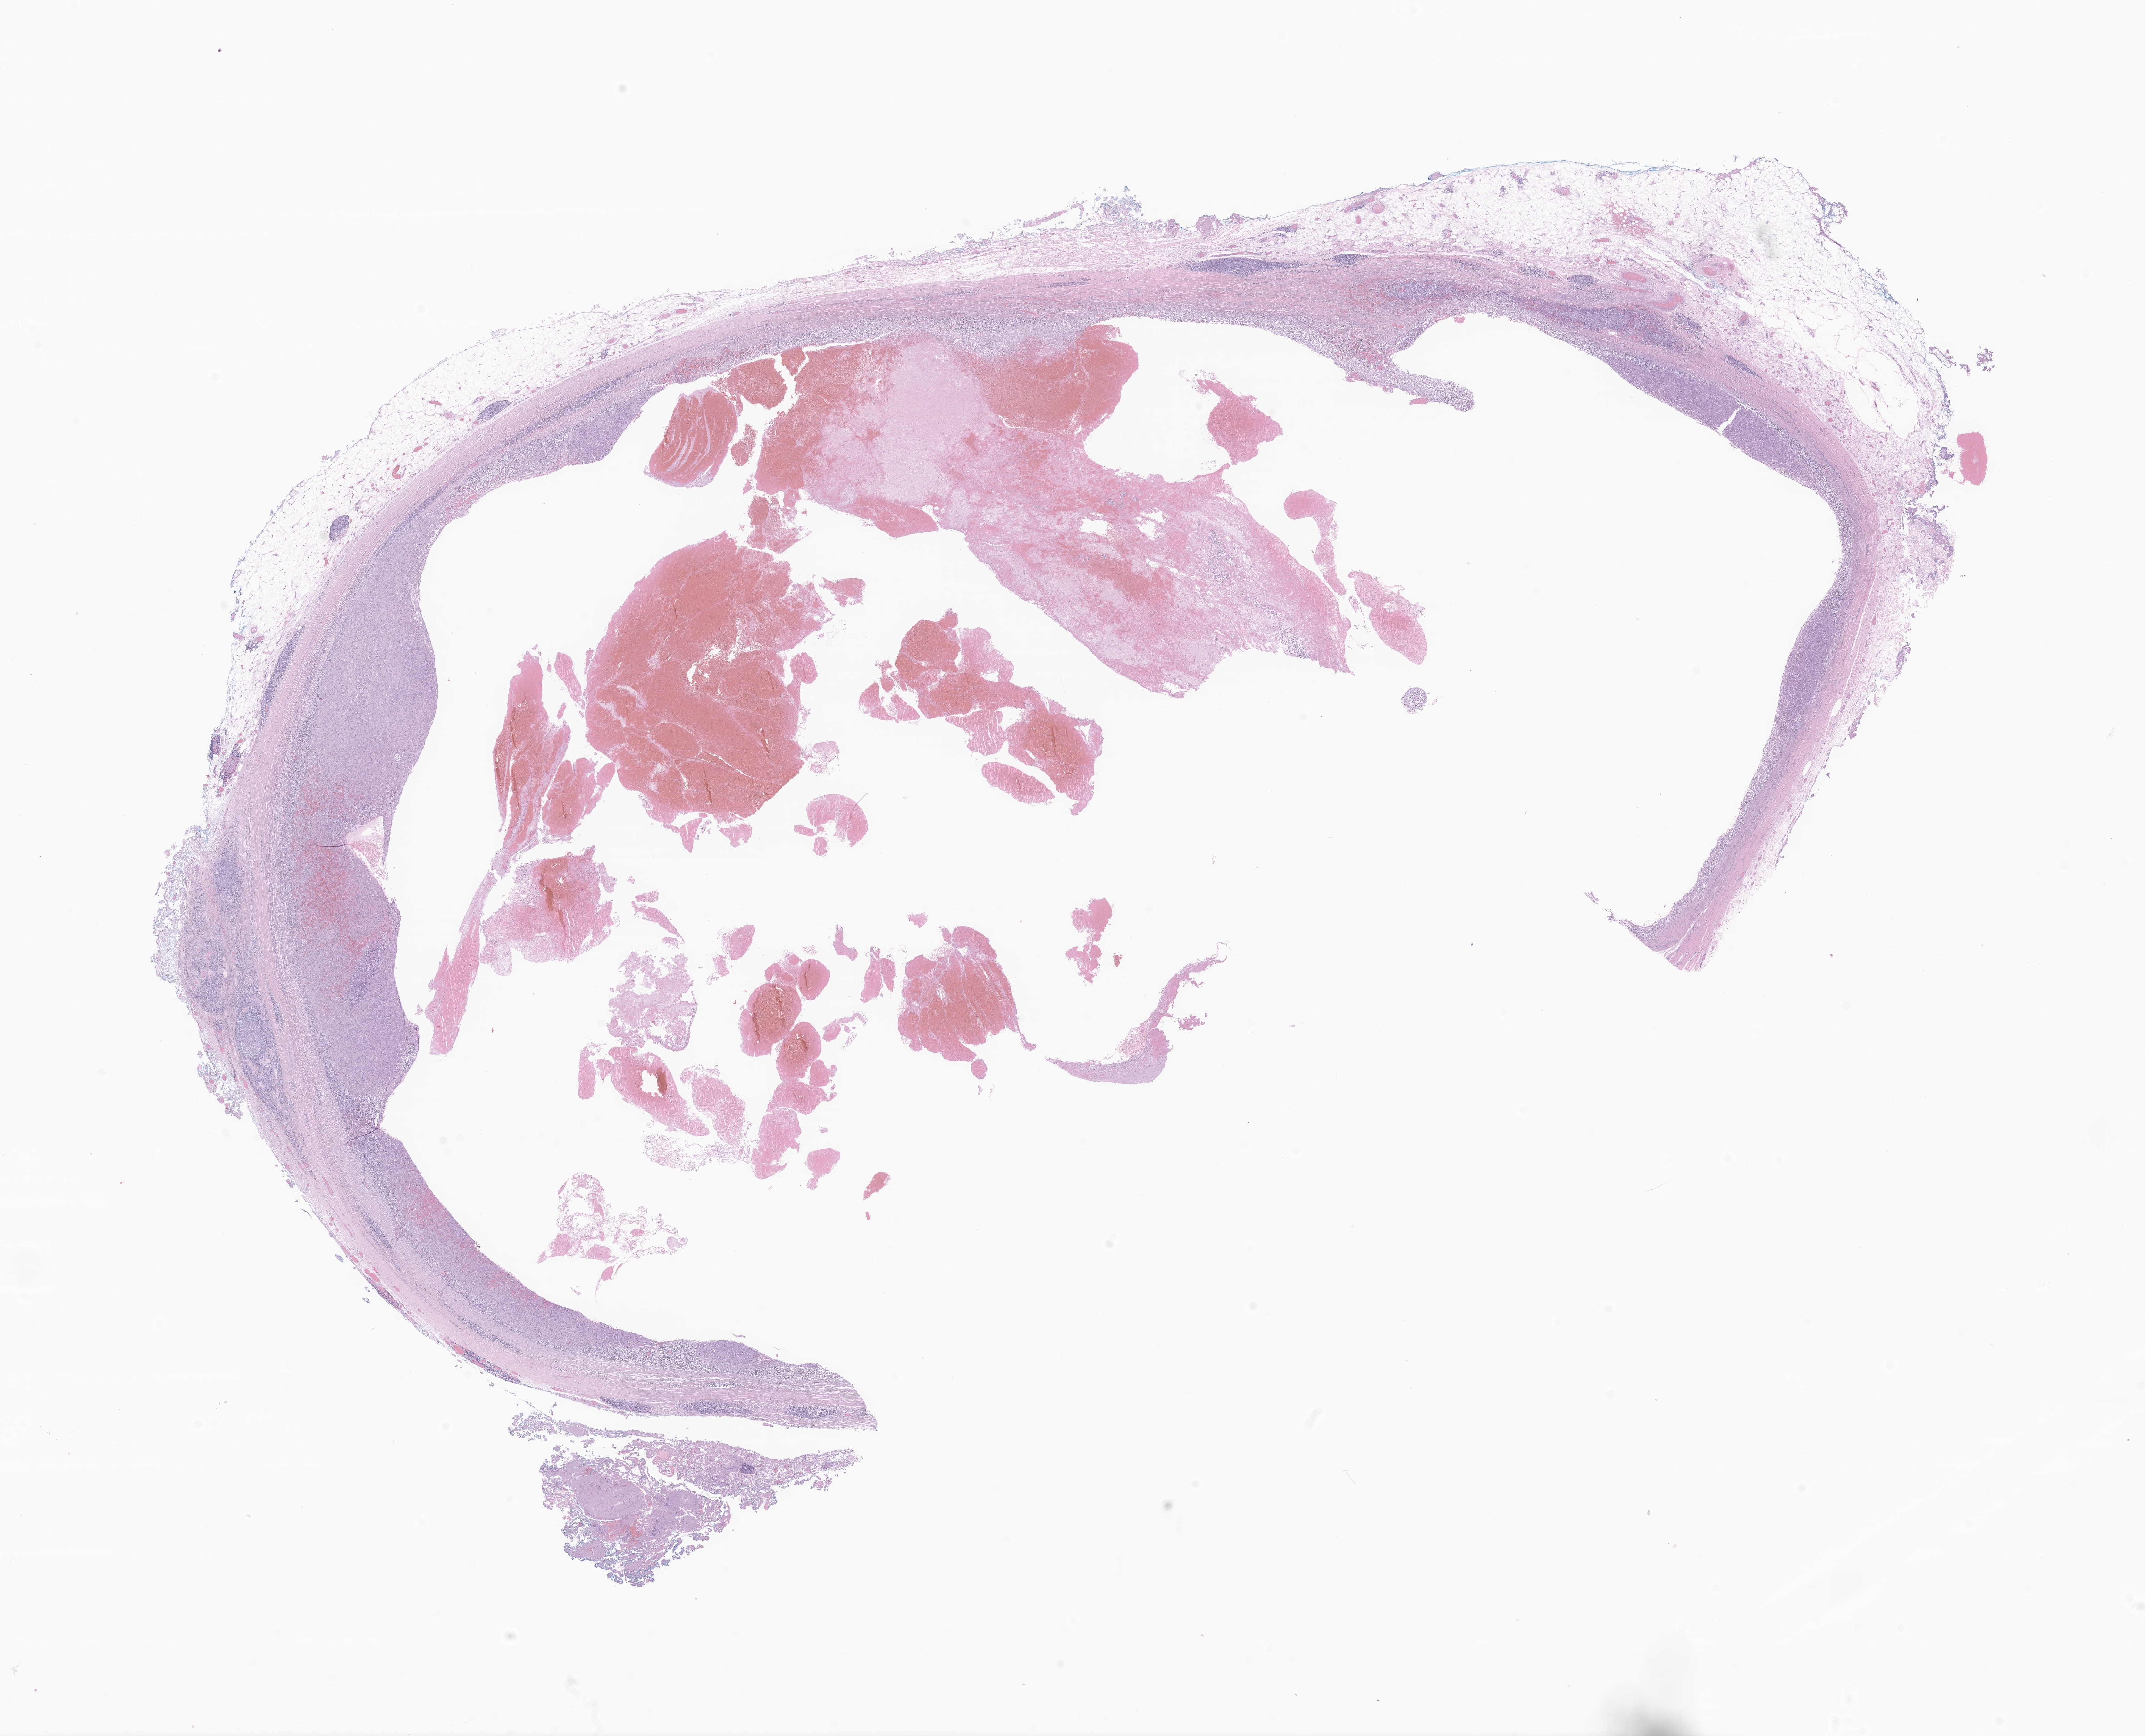
Whole-slide image, hematoxylin and eosin (H&E) stain of tumor tissue from the soft tissue of pelvis — low-resolution overview of the scanned area, about 26.0 x 21.1 mm. Formalin-fixed paraffin-embedded section. Patient: female, age 114 months (9 years 6 months).
• diagnosis (ICD-O-3 morphology term): Angiomatoid fibrous histiocytoma
• tissue or organ of origin (case record): connective, subcutaneous and other soft tissues of pelvis